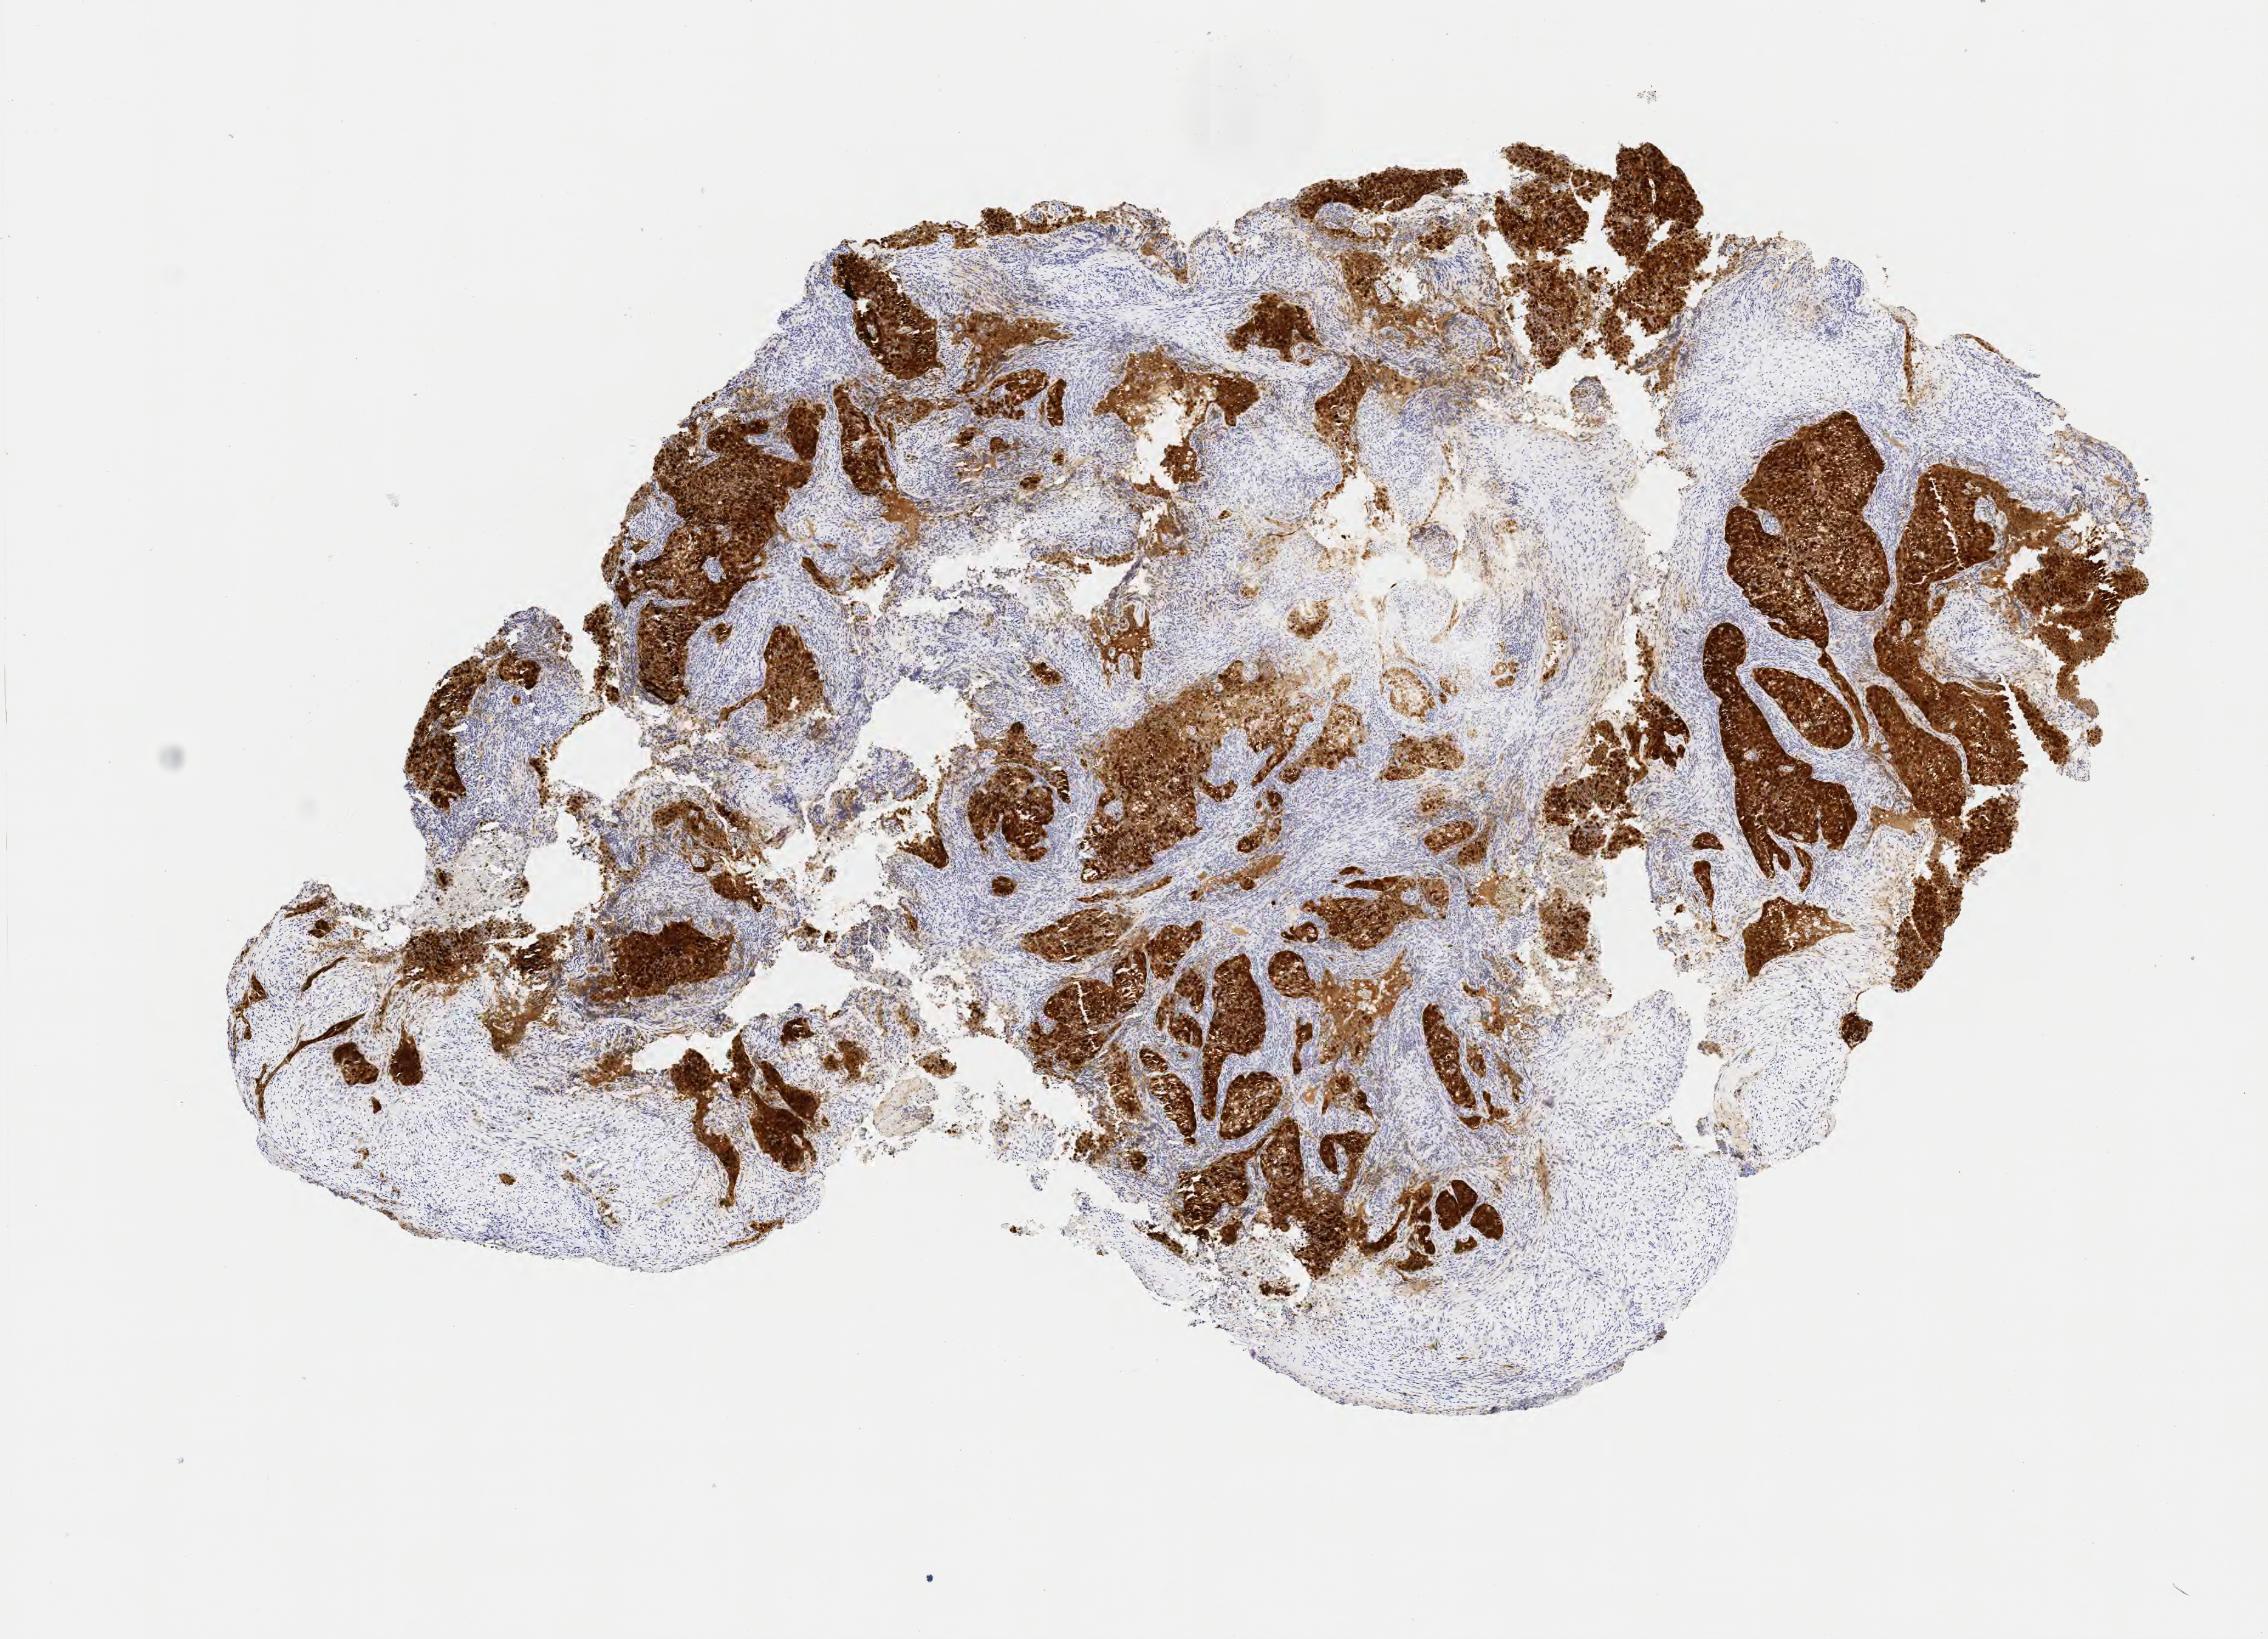
IHC for p16 (p16INK4a), whole-slide image, shown as a low-resolution overview of the whole scanned area (about 7.6 x 5.5 mm). Specimen: tumor tissue. Anatomic site: cervix. Female patient, age 39 years.
• histologic diagnosis: Squamous cell carcinoma, large cell, nonkeratinizing, NOS